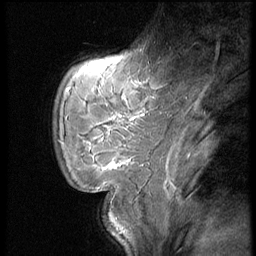
Breast MRI (dynamic contrast-enhanced), one sagittal slice. Slice 14 of 62 in the series (ordered by position). Dynamic contrast-enhanced series, image 2 of 4 at this slice position (ordered by acquisition). 1.5 T. TE 4.2 ms, TR 9 ms. 2.5 mm slice thickness. 256 × 256 image matrix. Patient: female, 28 years. Case-level facts recorded for this patient, not image findings: setting: breast cancer imaged before/during neoadjuvant chemotherapy.
Structures marked on this image (semi-automatic segmentation, software-assisted and operator-edited):
- analysis volume of interest (the breast-tissue region the enhancement analysis was run in; not a lesion): bounding box (x1, y1, x2, y2) in pixels: (56, 54, 150, 183)
- tumour enhancement mask (voxels above the 140 % enhancement threshold inside the analysis volume of interest): (85, 118, 135, 169)